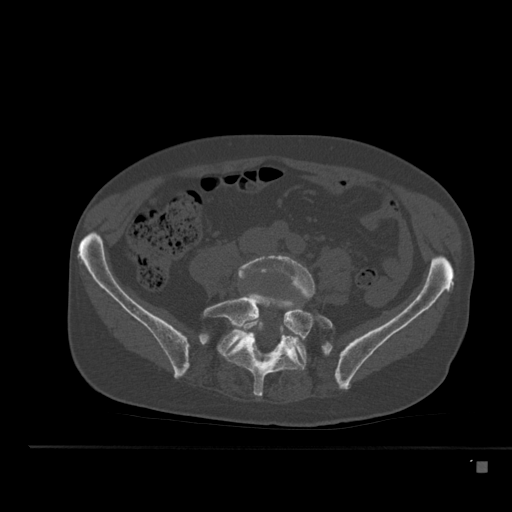
CT including the spine, one axial slice; slice 128 of 517 in the series (ordered by position); reconstruction kernel Br40s; 120 kVp; bone window (W 1800 / L 400 HU); 1.5 mm slice thickness; 512 × 512 image matrix, field of view 408 × 408 mm. Patient: male, 70 years. From the clinical record (not read from this slice): primary cancer: renal.
Annotated regions visible in this slice (semi-automatically segmented with operator editing):
- L4 vertebra: box from (x=238, y=255) to (x=315, y=335) px
- L5 vertebra: (x=203, y=293)–(x=333, y=397)